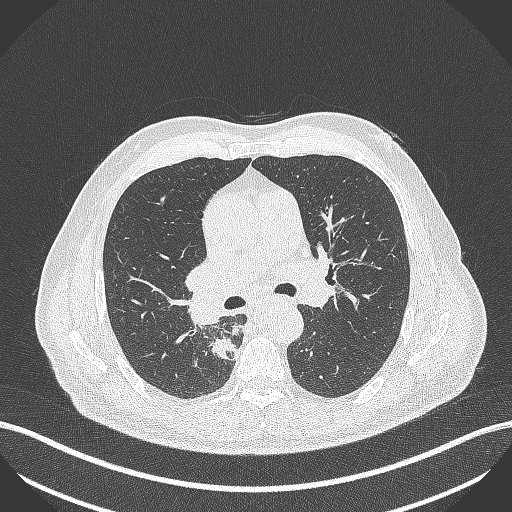
Chest CT, one axial slice. Position 279 of 451 along the scan axis. 100 kVp. Lung window (W 1500 / L -600 HU). 1 mm slice thickness. 512 × 512 image matrix, field of view 400 × 400 mm. Patient: male, 61 years. From the clinical record (not read from this slice): clinical TNM (as recorded): T1 N0 M0.
Annotated regions visible in this slice (rectangle marked by the reading radiologist):
- lung tumour (recorded histology: small cell carcinoma): bounding box <206,336,240,368> (left, top, right, bottom; pixels)